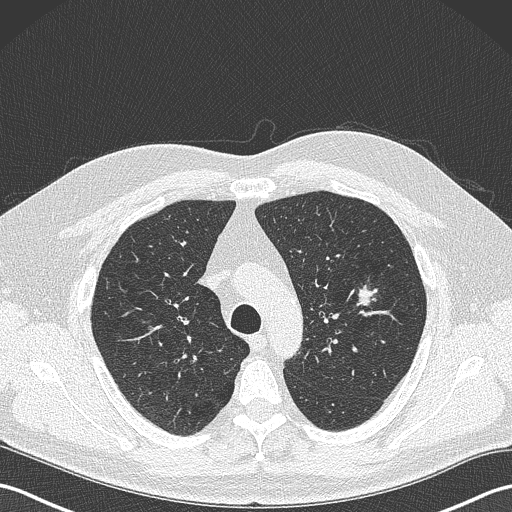
Low-dose screening chest CT, one axial slice; position 253 of 343 along the scan axis; reconstruction kernel B50f; 120 kVp; lung window (W 1500 / L -600 HU); 1 mm slice thickness; 512 × 512 image matrix.
Outlined on this slice (expert manual segmentation):
- lesion 1 (tumor, upper lobe of left lung): box from (x=356, y=285) to (x=378, y=306) px